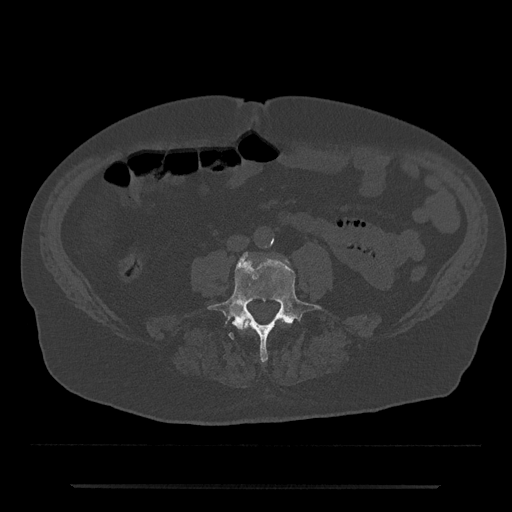
CT including the spine, one axial slice; position 357 of 797 along the scan axis; 120 kVp; bone window (W 1800 / L 400 HU); 0.5 mm slice thickness; 512 × 512 image matrix, field of view 434 × 434 mm. Male patient, age 80 years. From the clinical record (not read from this slice): primary cancer: prostate; vertebrae with lytic lesions (as recorded): L1, T11.
Outlined on this slice (semi-automatically segmented with operator editing):
- L3 vertebra: bounding box (x1, y1, x2, y2) in pixels: (242, 319, 289, 329)
- L4 vertebra: (208, 252, 321, 362)